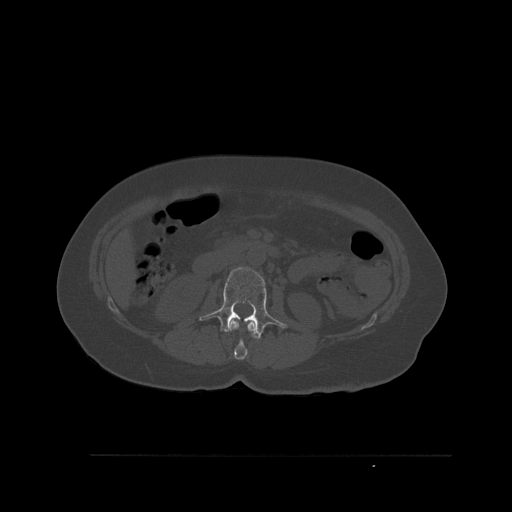
CT including the spine, one axial slice. Bone window (W 1800 / L 400 HU). 1.5 mm slice thickness. 512 × 512 image matrix. Patient: female, 73 years. From the clinical record (not read from this slice): primary cancer: breast.
Annotated regions visible in this slice (semi-automatically segmented with operator editing):
- L1 vertebra: bounding box [x1, y1, x2, y2] px = [229, 319, 256, 360]
- L2 vertebra: [199, 267, 287, 339]